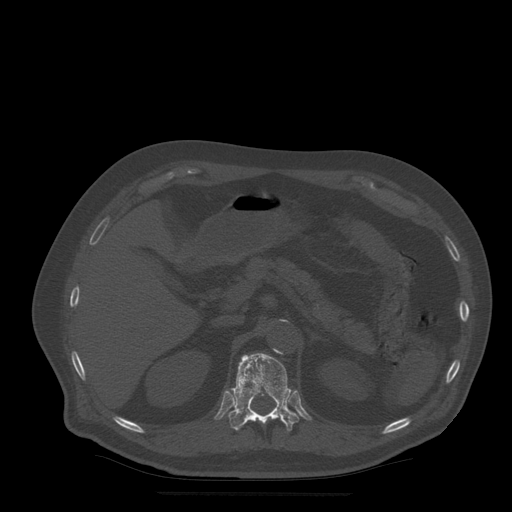
CT including the spine, one axial slice. Slice 222 of 522 in the series (ordered by position). Bone window (W 1800 / L 400 HU). 1.25 mm slice thickness. 512 × 512 image matrix, field of view 420 × 420 mm. Patient age 72 years. Case-level facts recorded for this patient, not image findings: primary cancer: prostate.
Outlined on this slice (semi-automatically segmented with operator editing):
- T12 vertebra: bounding box [x1, y1, x2, y2] px = [229, 353, 300, 432]